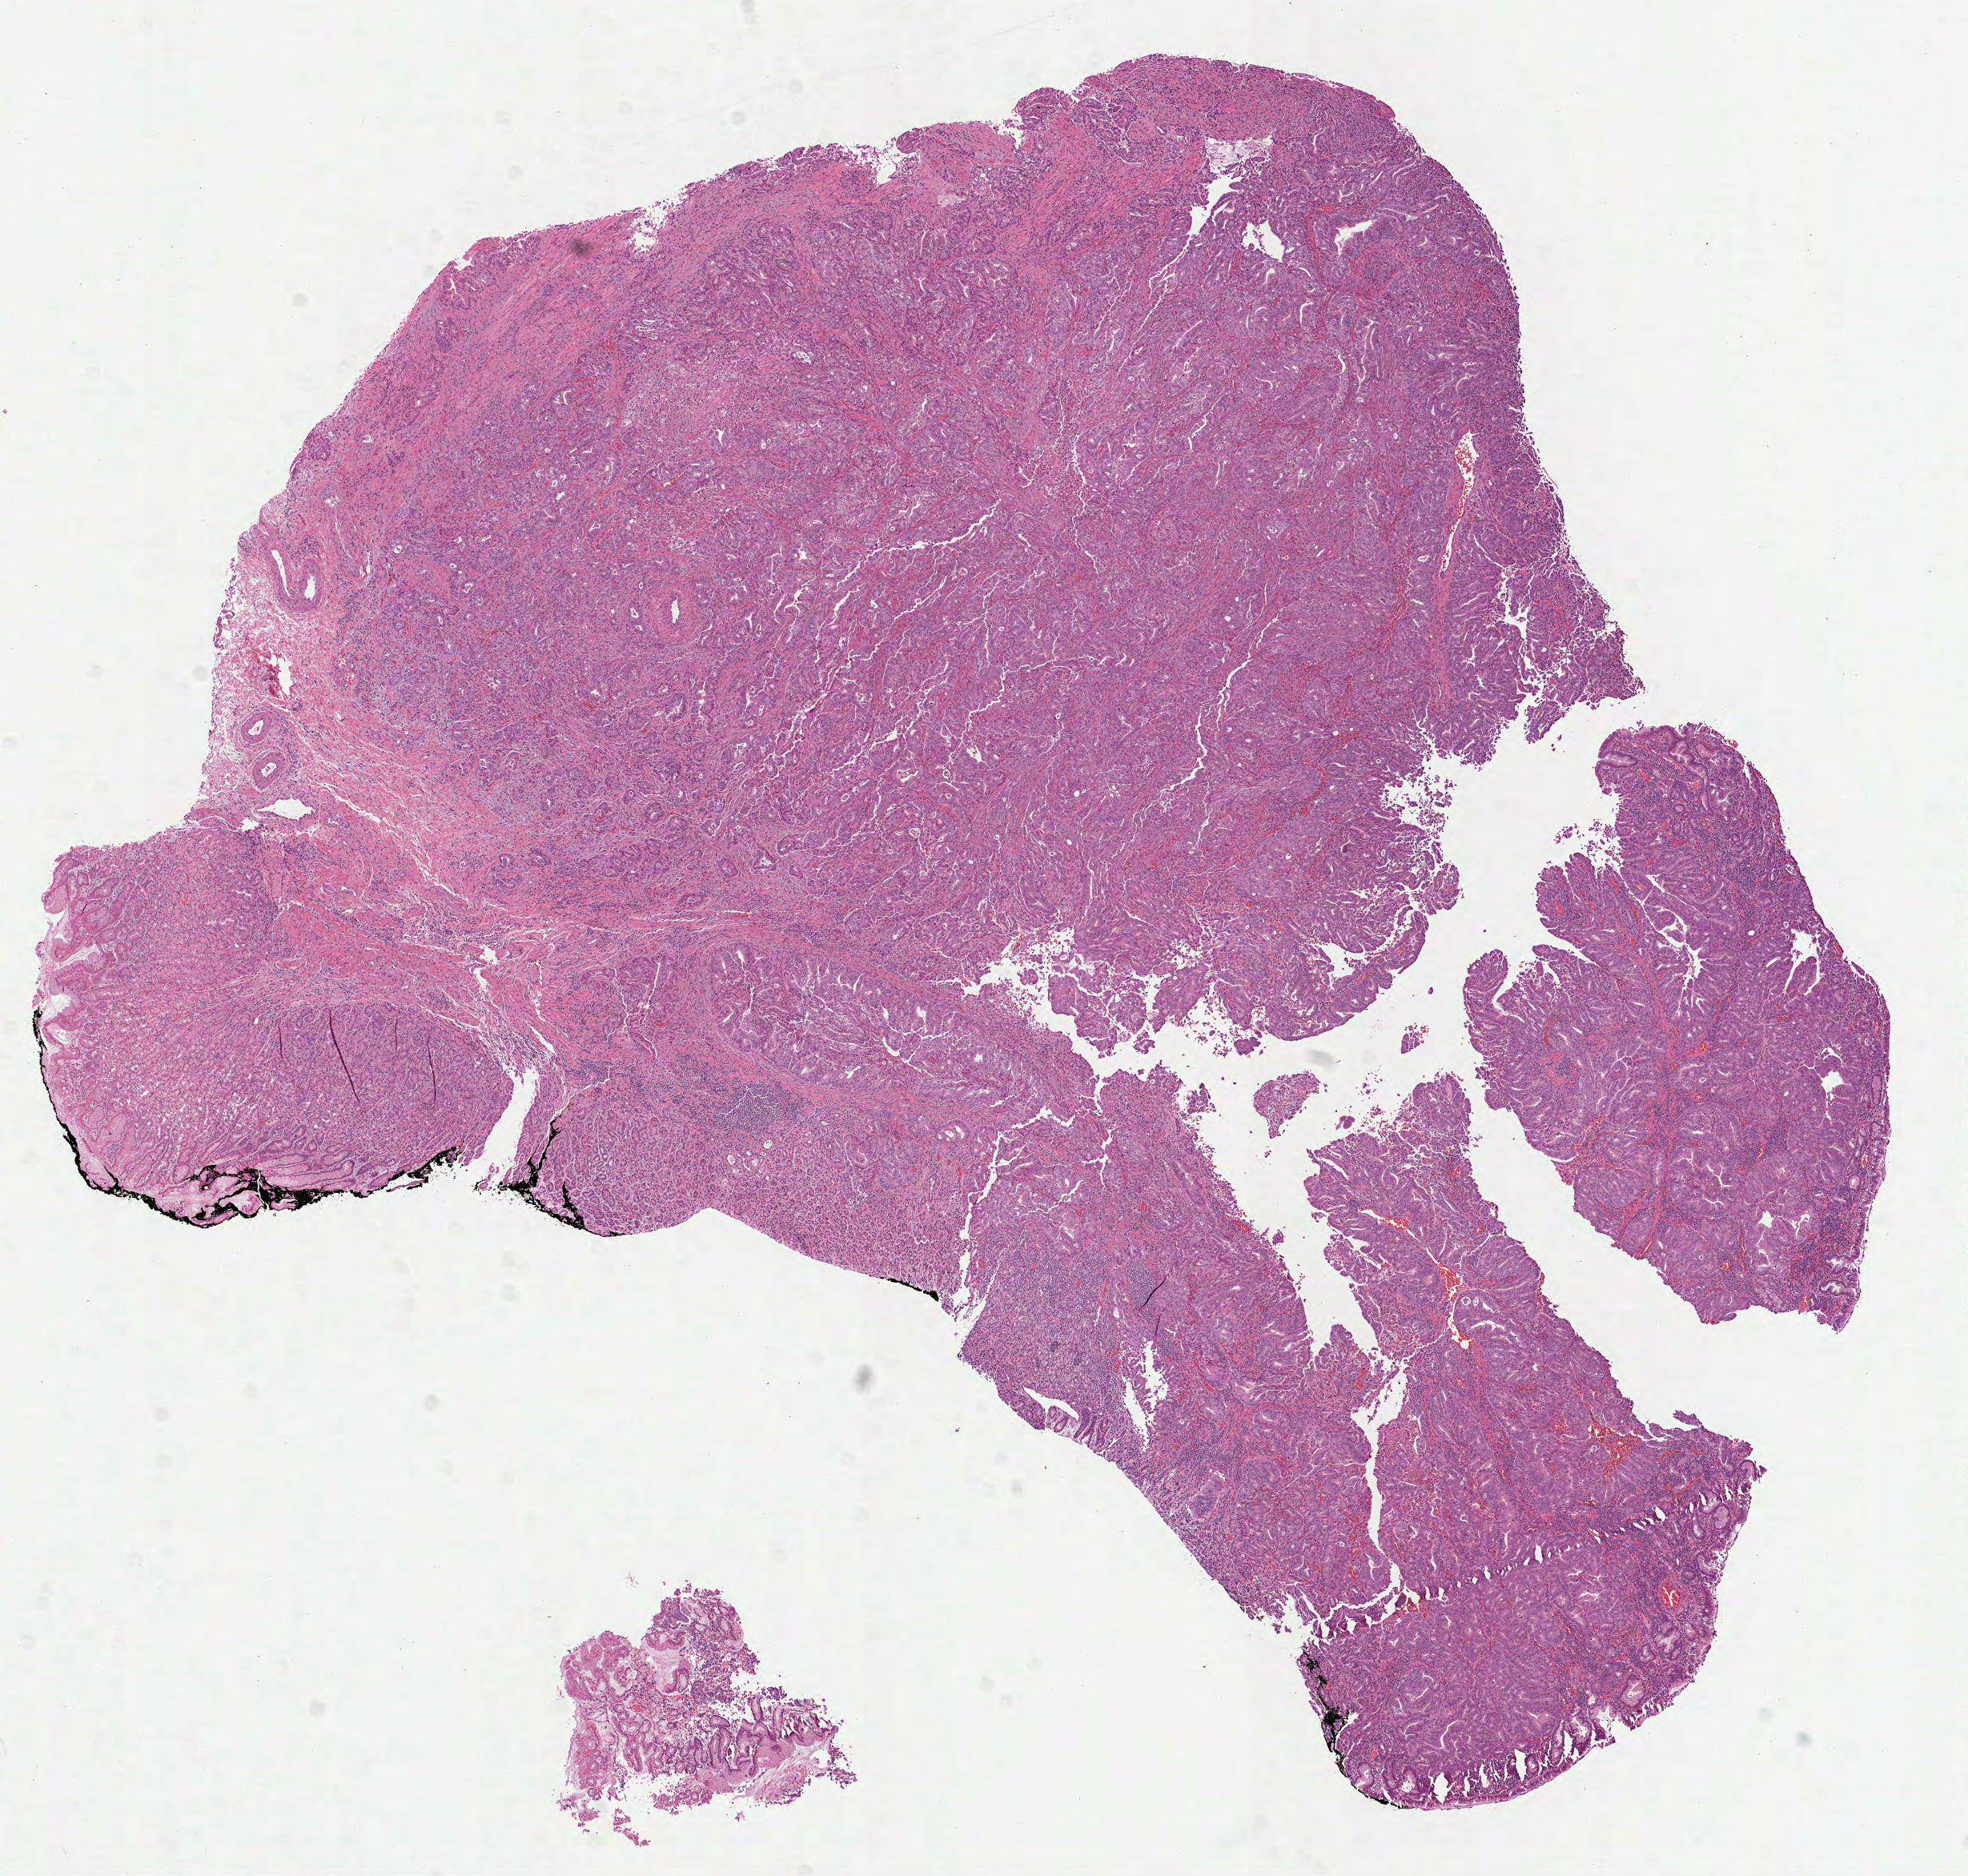
H&E-stained whole-slide image, shown as a low-resolution overview of the whole scanned area (about 9.9 x 9.4 mm, from a 40x scan). Formalin-fixed paraffin-embedded (FFPE) diagnostic section. Stomach, primary tumour sample. Patient: male, age at initial diagnosis 62 years. Histologic grade: G2 (moderately differentiated).
Lymph nodes positive (case pathology): 2 of 7 examined. AJCC pathologic stage: IIB (7th edition). Histologic diagnosis: Adenocarcinoma, NOS. TNM: T3 N1 MX.